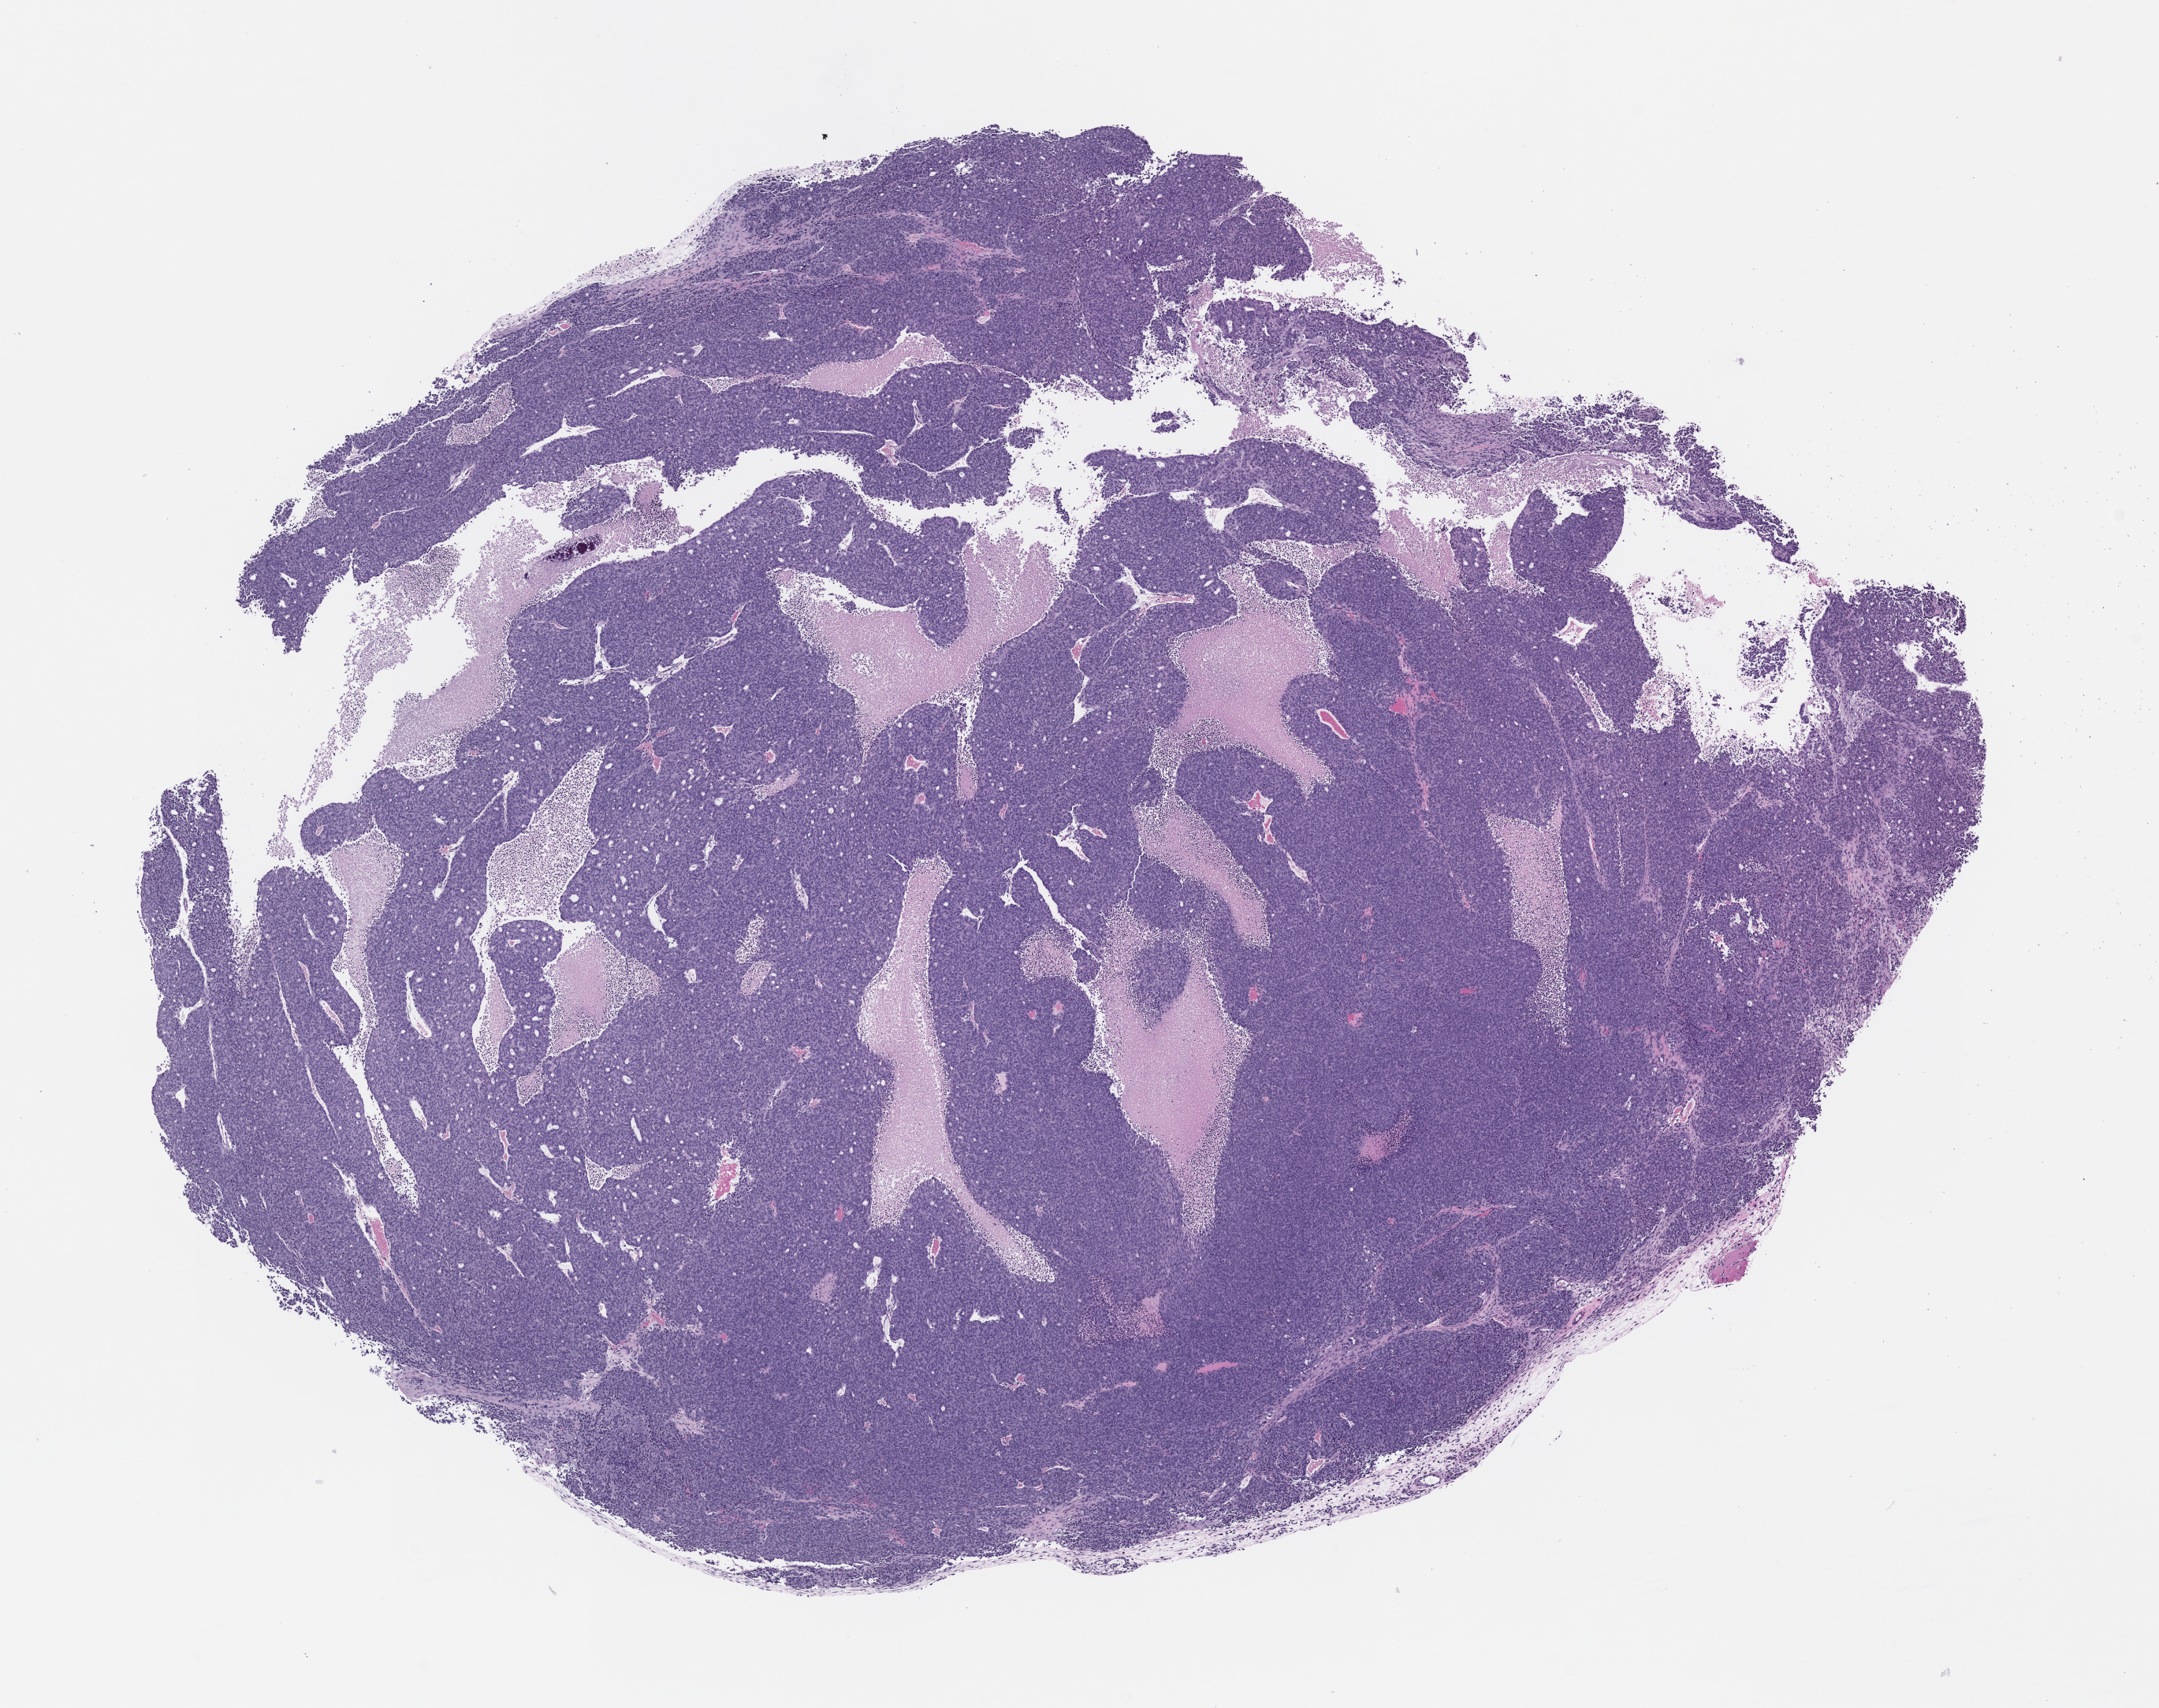
Whole-slide image, H&E: patient-derived xenograft (human tumor grown in a mouse), passage 2 — low-resolution overview of the scanned area, about 11.0 x 8.7 mm, formalin-fixed, paraffin-embedded (FFPE) tissue, tumor site category: cervix.
• originating patient diagnosis: Cervical Adenocarcinoma